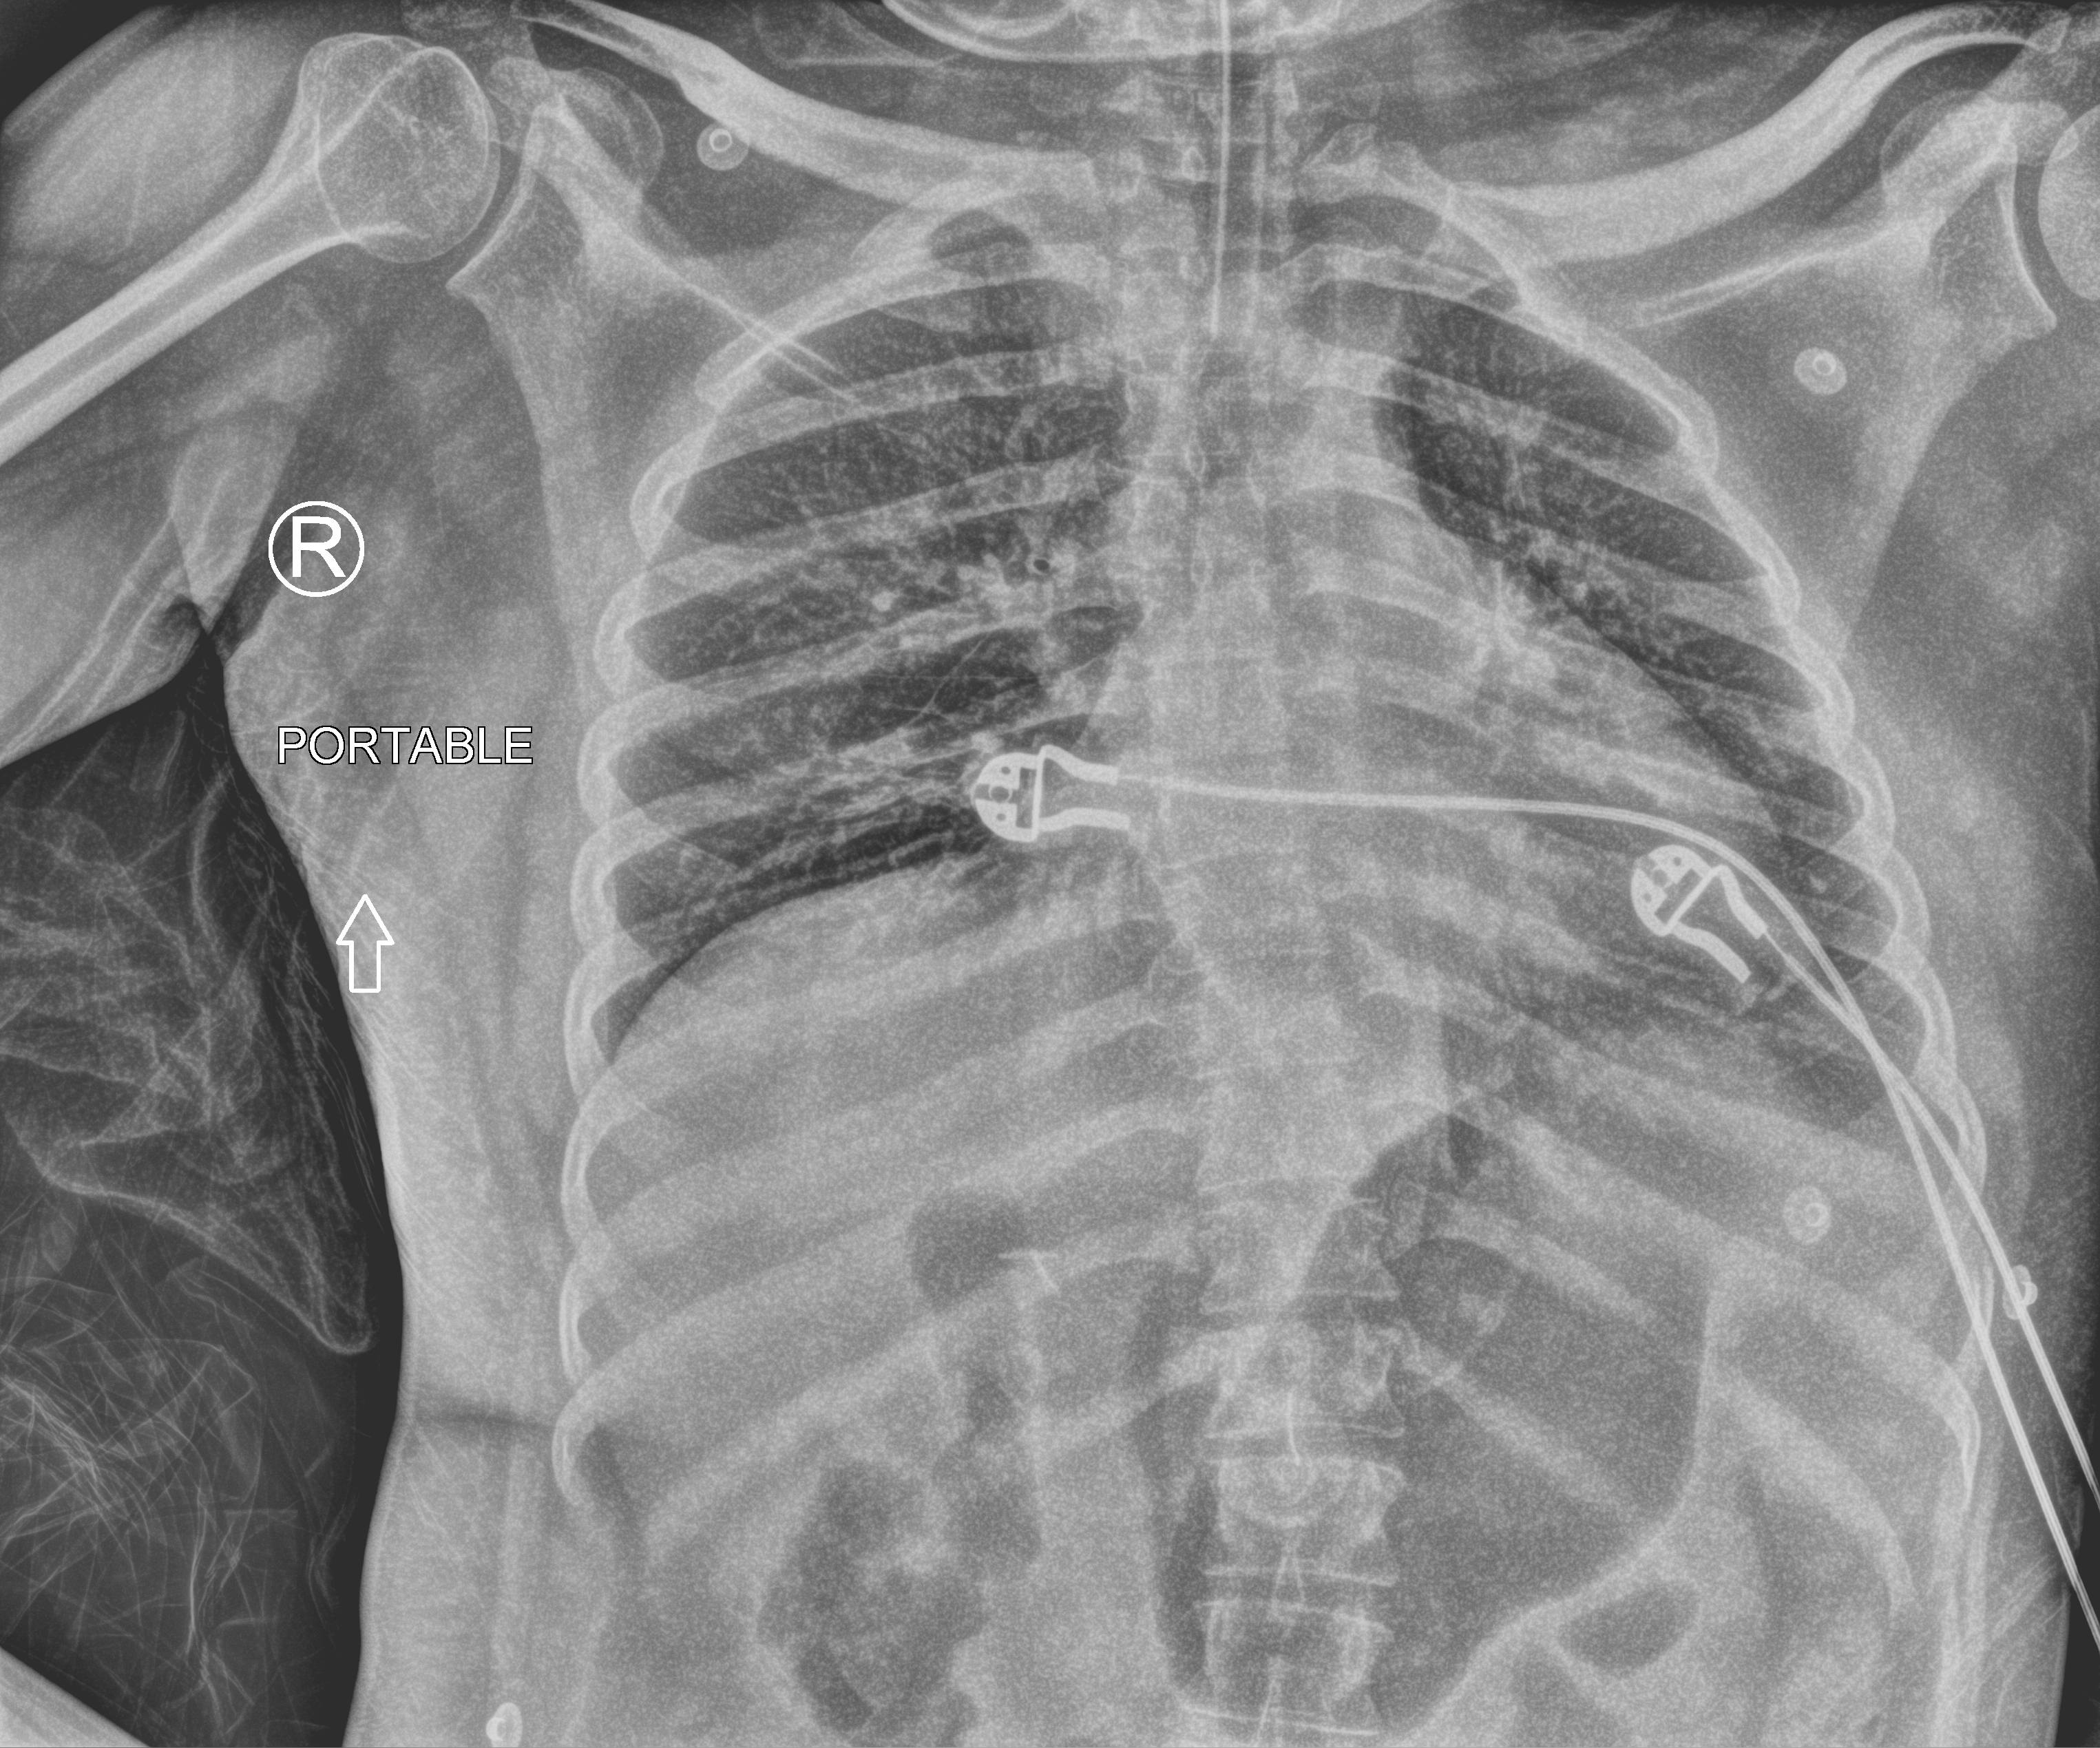
Portable chest radiograph; anteroposterior (AP) projection. Male patient hospitalised with COVID-19, age 18–59 years.
Hospital-stay facts (about this admission, not read from this image; timing relative to this image not recorded): mechanically ventilated during this hospital stay: no; admitted to intensive care during this hospital stay: no.